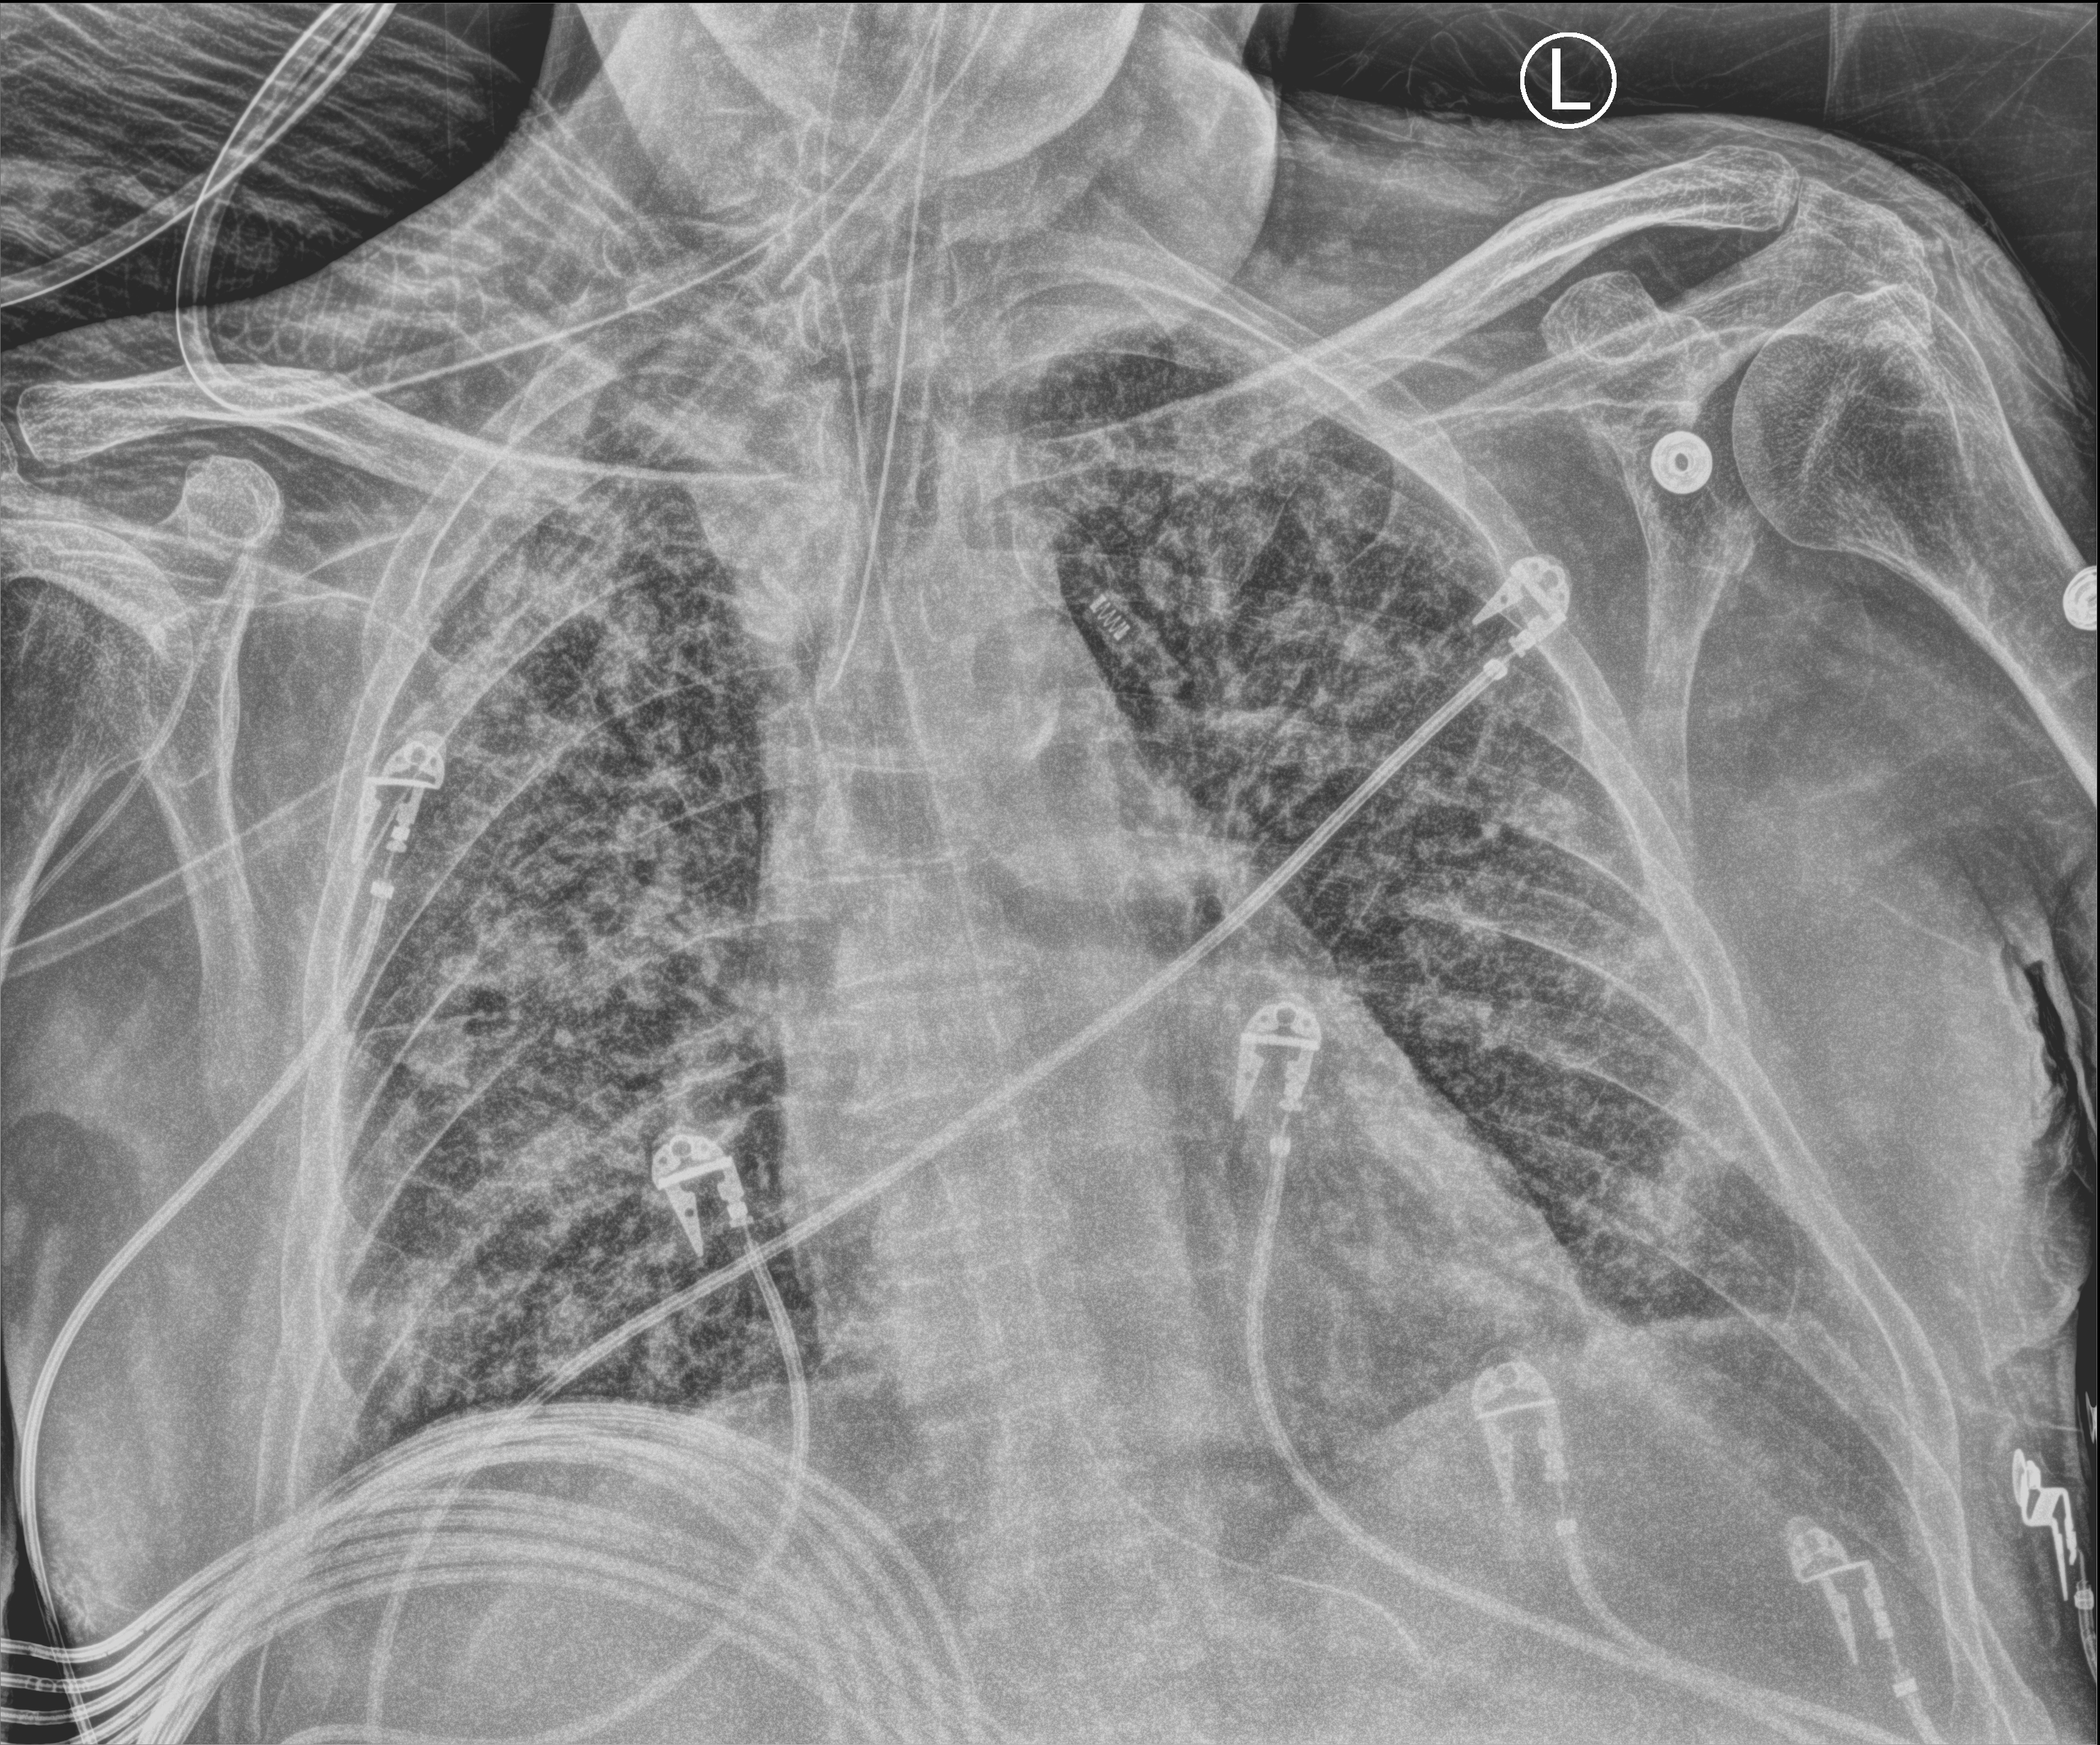
Portable chest radiograph, anteroposterior (AP) projection. Male patient hospitalised with COVID-19, age 60–74 years.
From the hospital-stay record, not from the radiograph (when in the stay this image was taken is not recorded): diabetes (admission record): no.